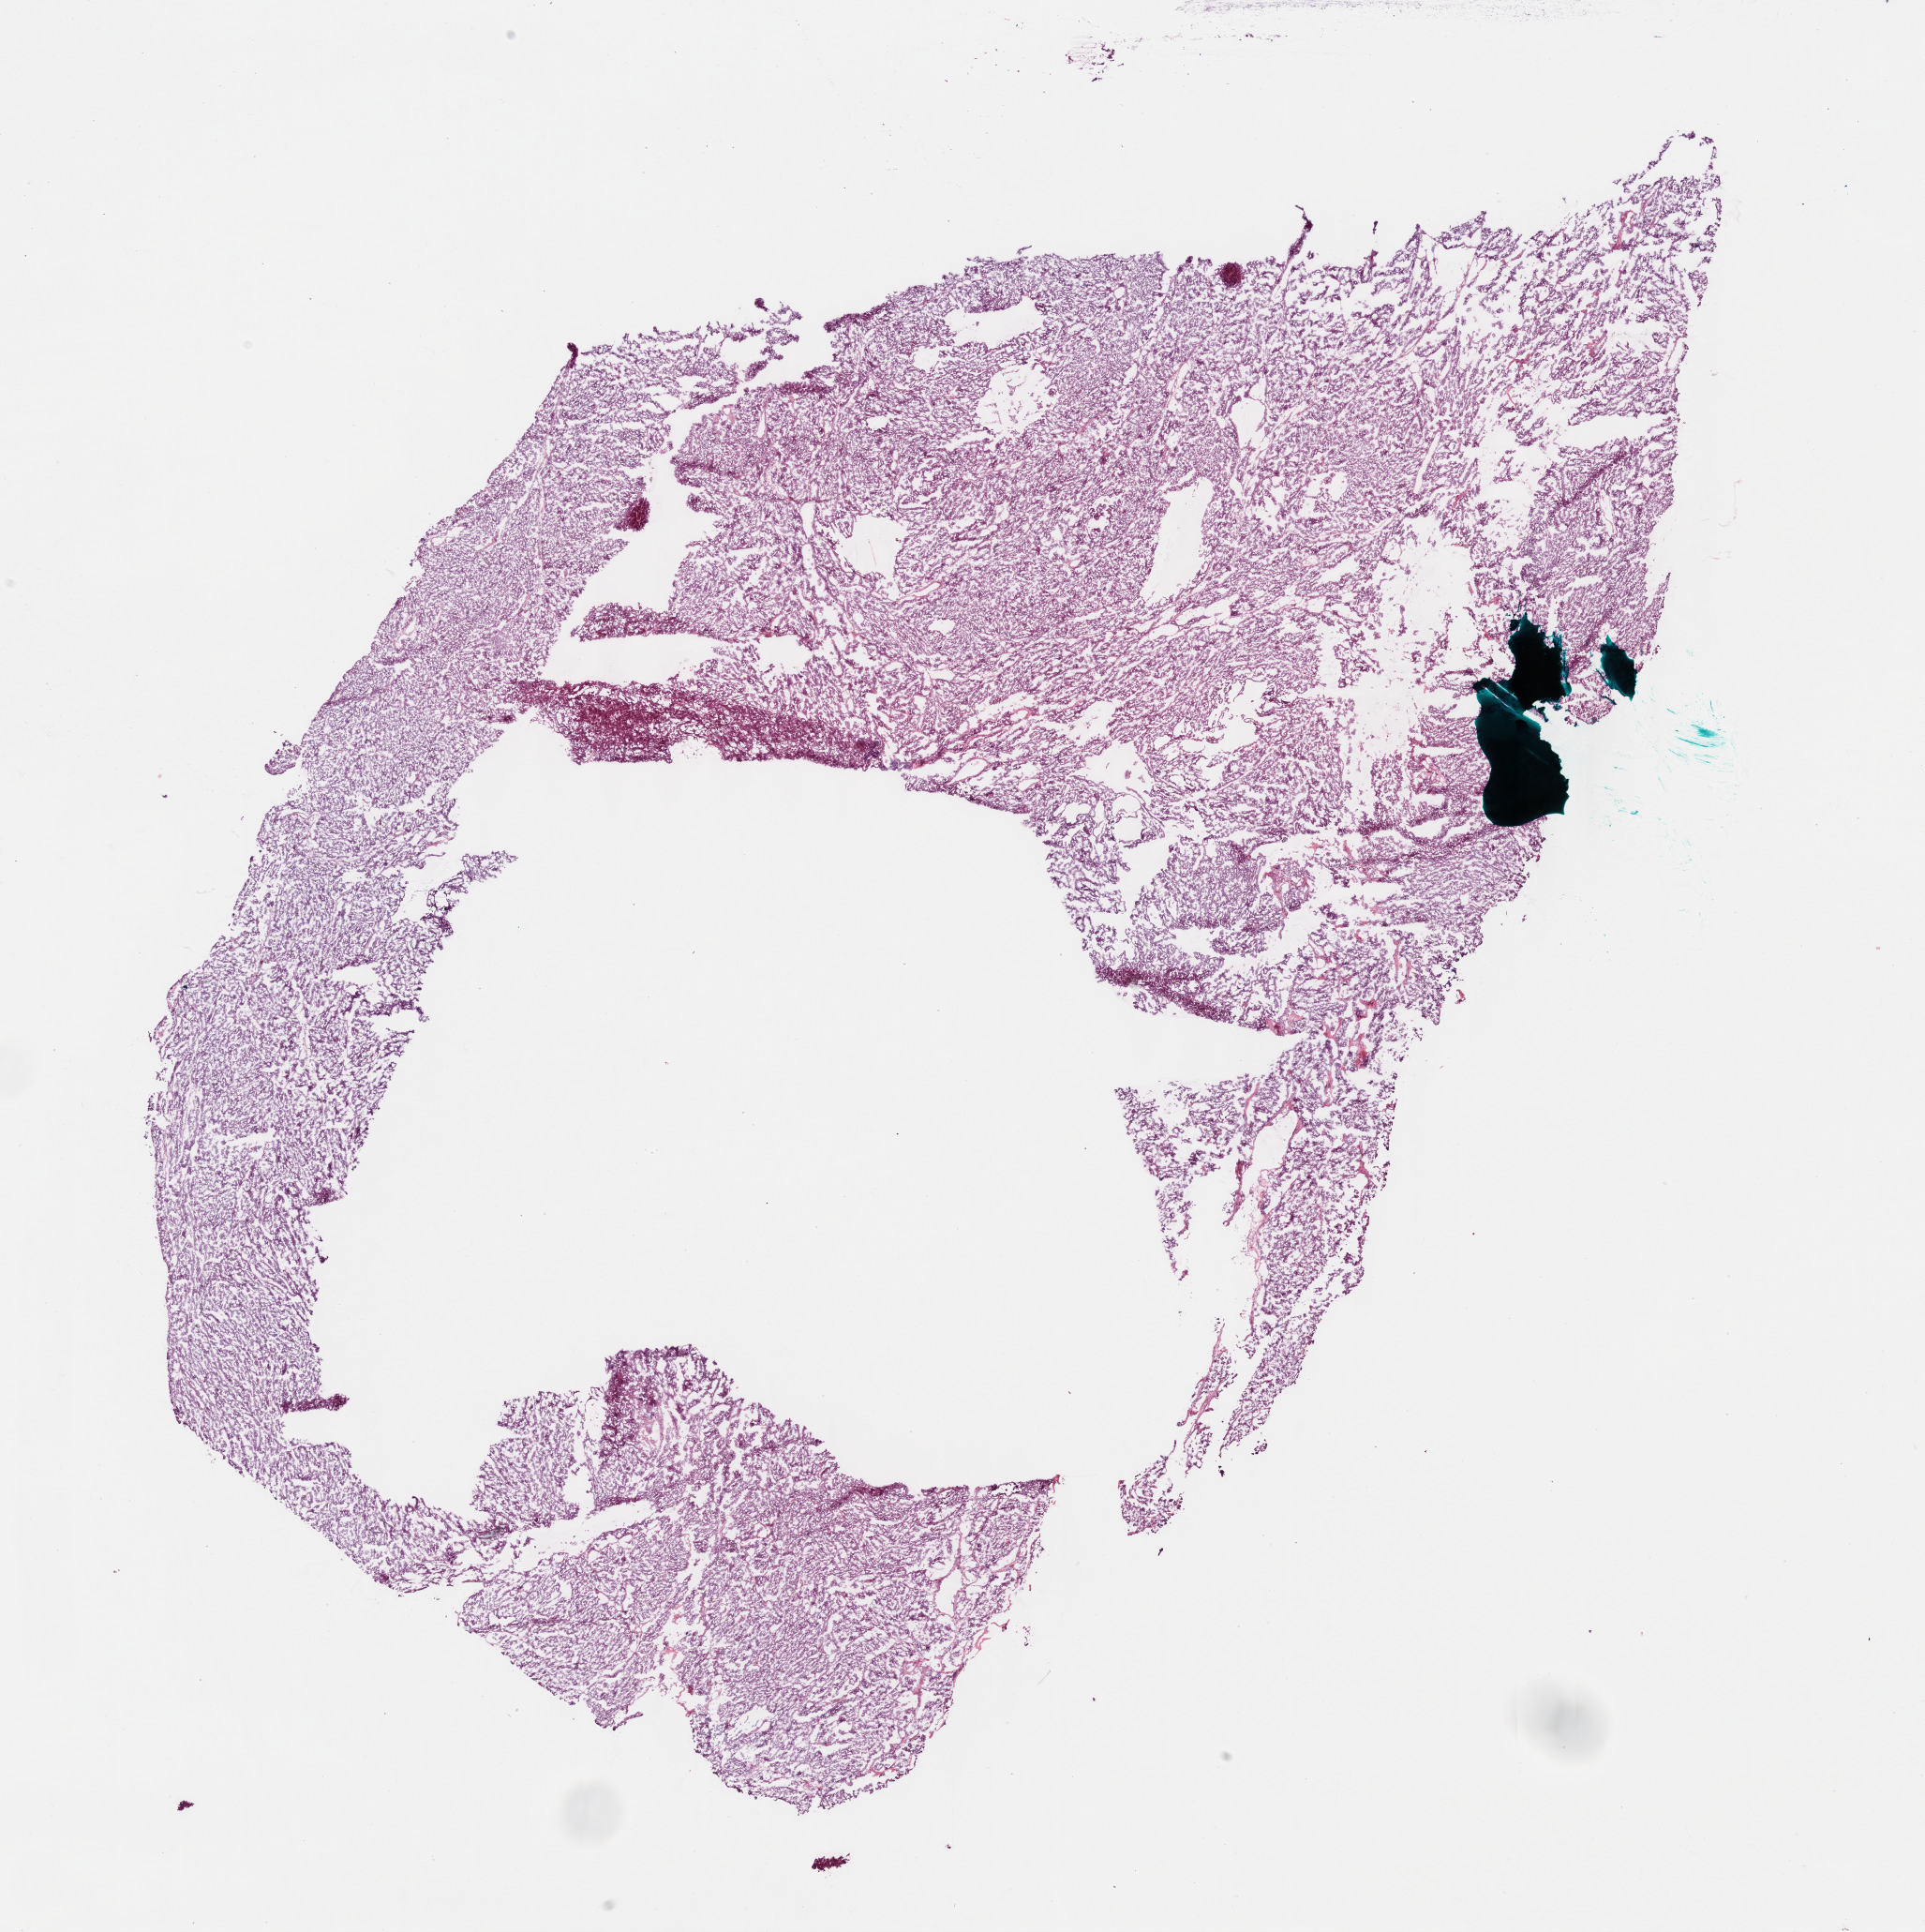
Hematoxylin and eosin (H&E) stained whole-slide image — a low-resolution overview of the entire scanned area, about 16.6 x 16.7 mm (from a 40x scan). Frozen section from the bottom of the tissue portion. Ovary, primary tumour sample. Patient: female, age at initial diagnosis 49 years. Histologic grade: G3 (poorly differentiated). Slide review estimates, as recorded: tumour cells 95%, tumour nuclei 98%, normal cells 0%, stromal cells 5%, necrosis 0%.
FIGO stage: IIIC. Diagnosis: Serous cystadenocarcinoma, NOS. Laterality: bilateral.